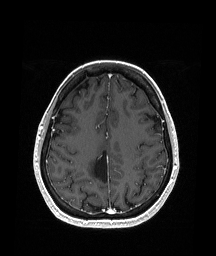
Brain MRI from a brain-tumour surgery series, one axial slice; position 65 of 151 along the scan axis; T1-weighted post-contrast; 1.05 mm slice thickness; 216 × 256 image matrix, field of view 211 × 250 mm. From the clinical record (not read from this slice): histopathology: Oligodendroglioma; WHO grade: 2; IDH mutation: yes; tumour location: Right Parietal.
Annotated regions visible in this slice (manually delineated by an expert):
- previous resection cavity: bounding box (x1, y1, x2, y2) in pixels: (94, 149, 109, 183)